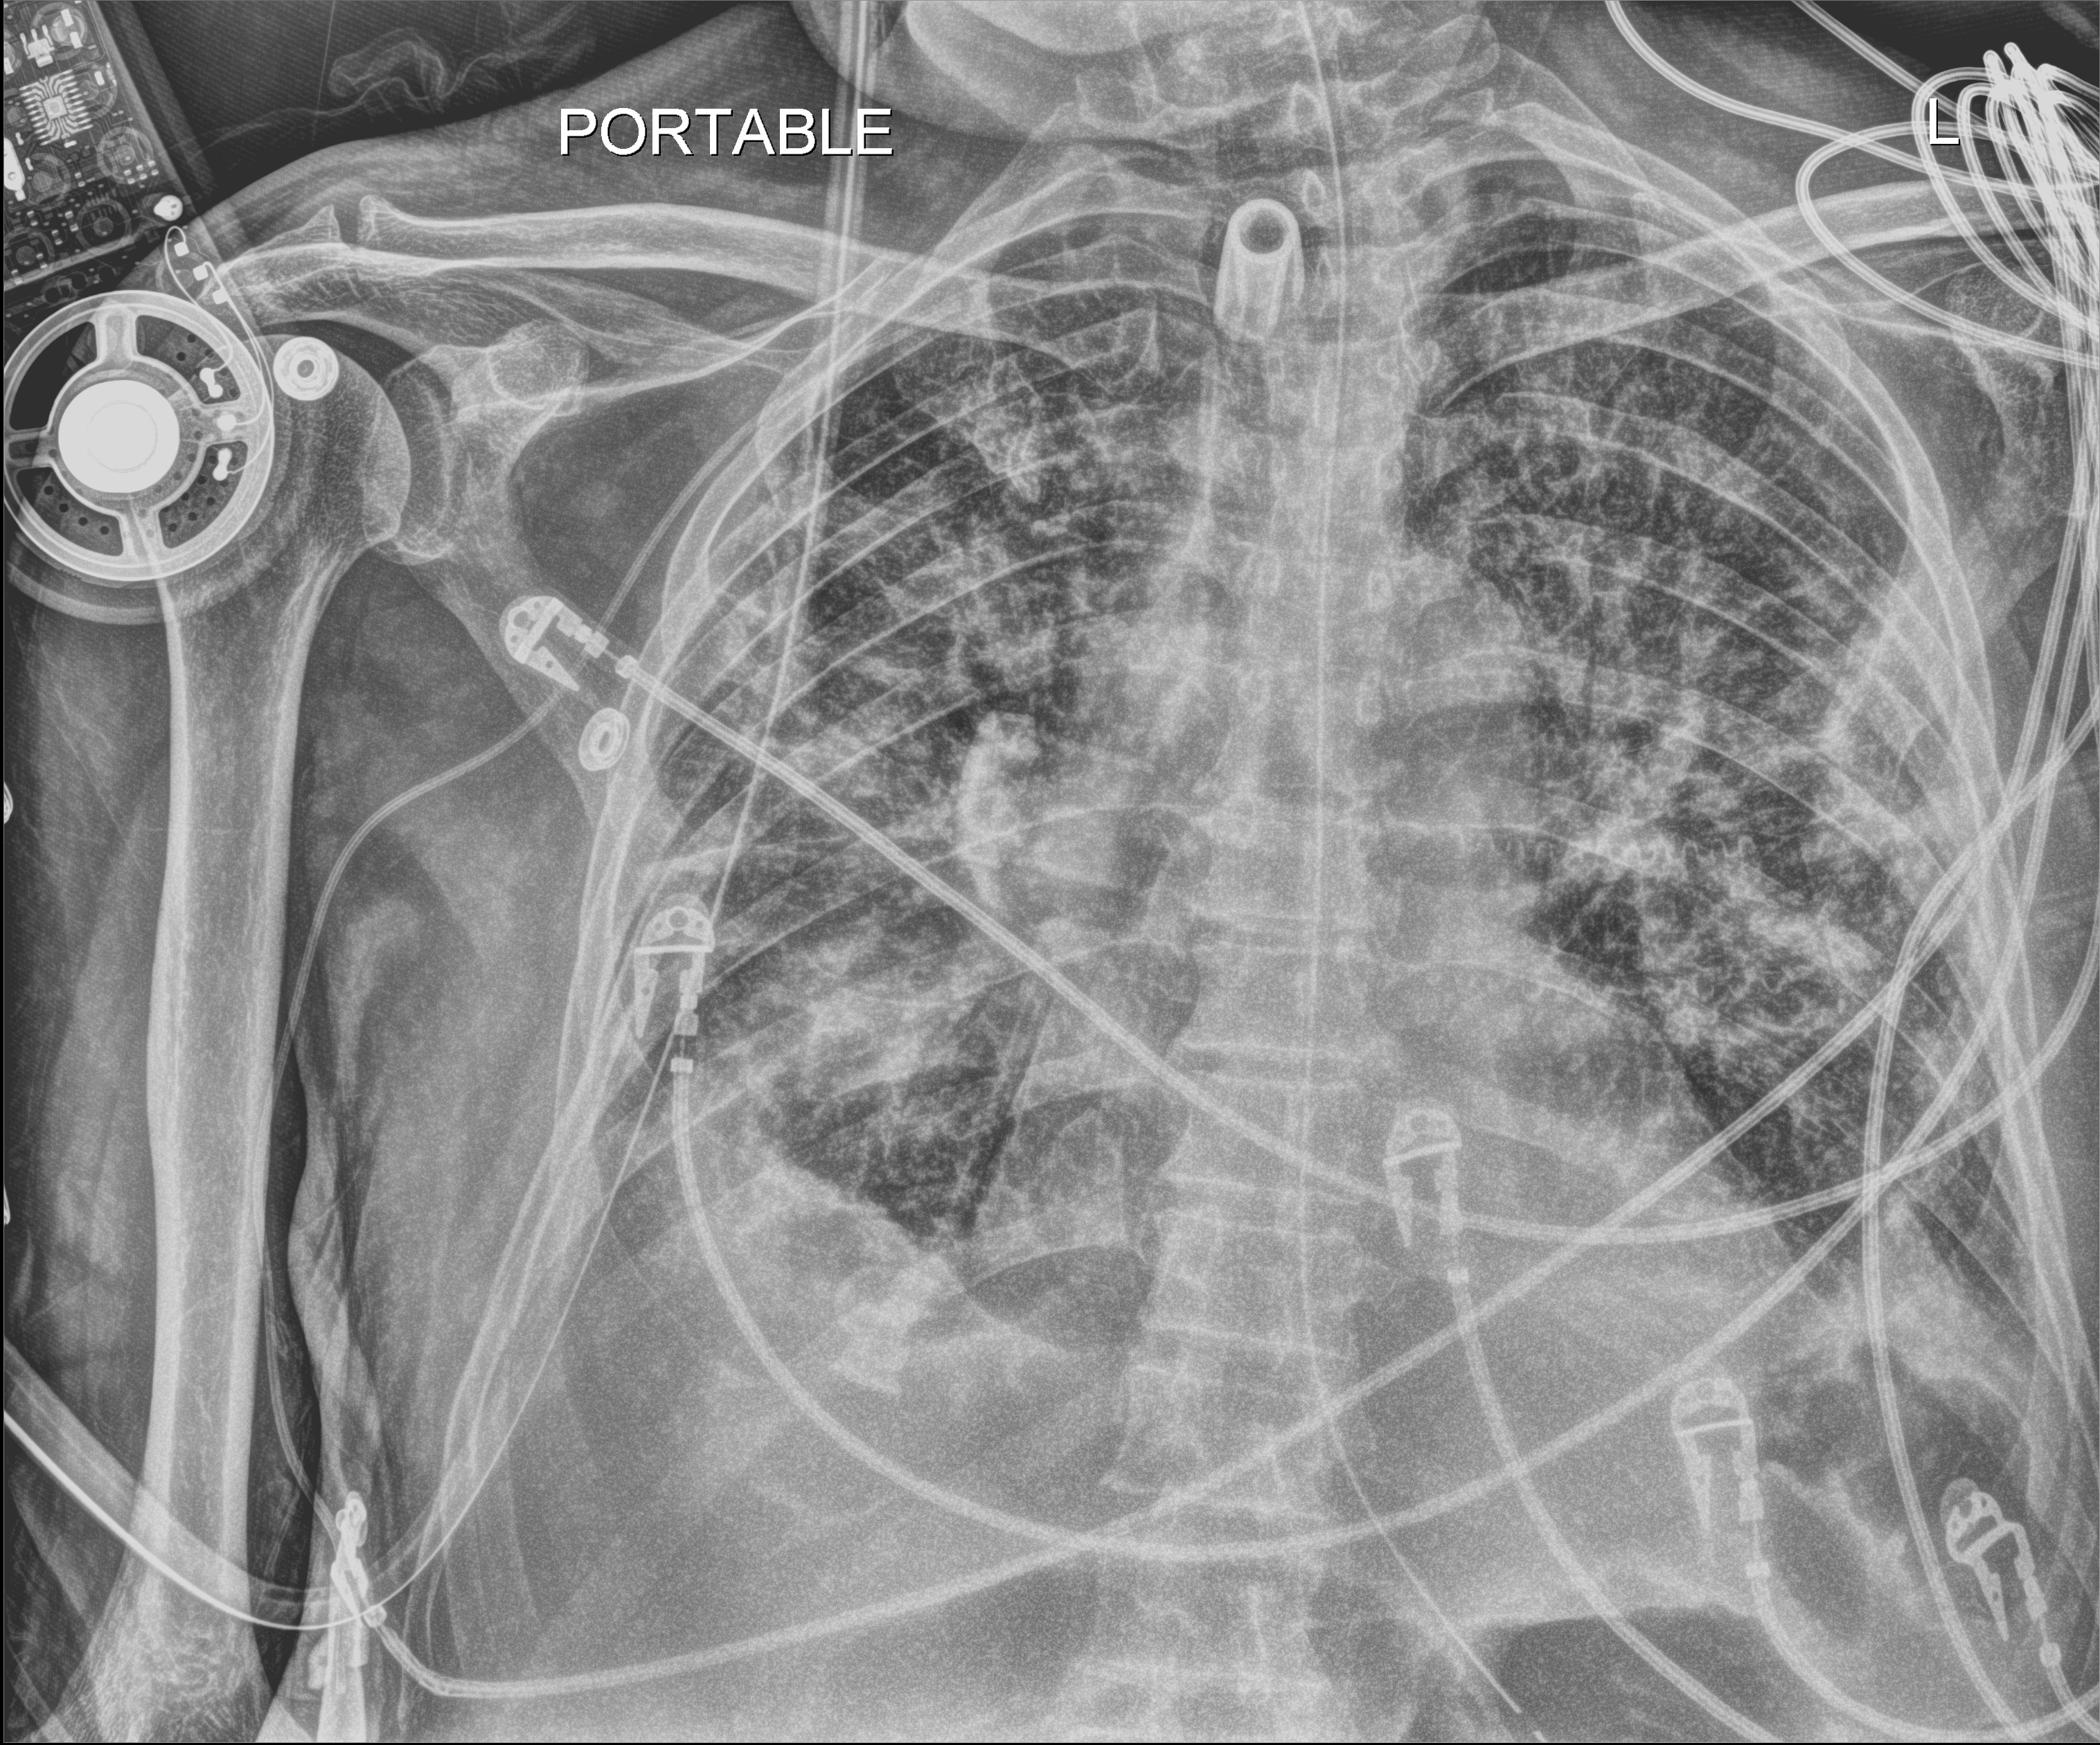
Bedside chest radiograph (digital radiography); anteroposterior (AP) projection. Male patient hospitalised with COVID-19, age 75–90 years.
From the hospital-stay record, not from the radiograph (when in the stay this image was taken is not recorded):
- length of hospital stay: 70 days